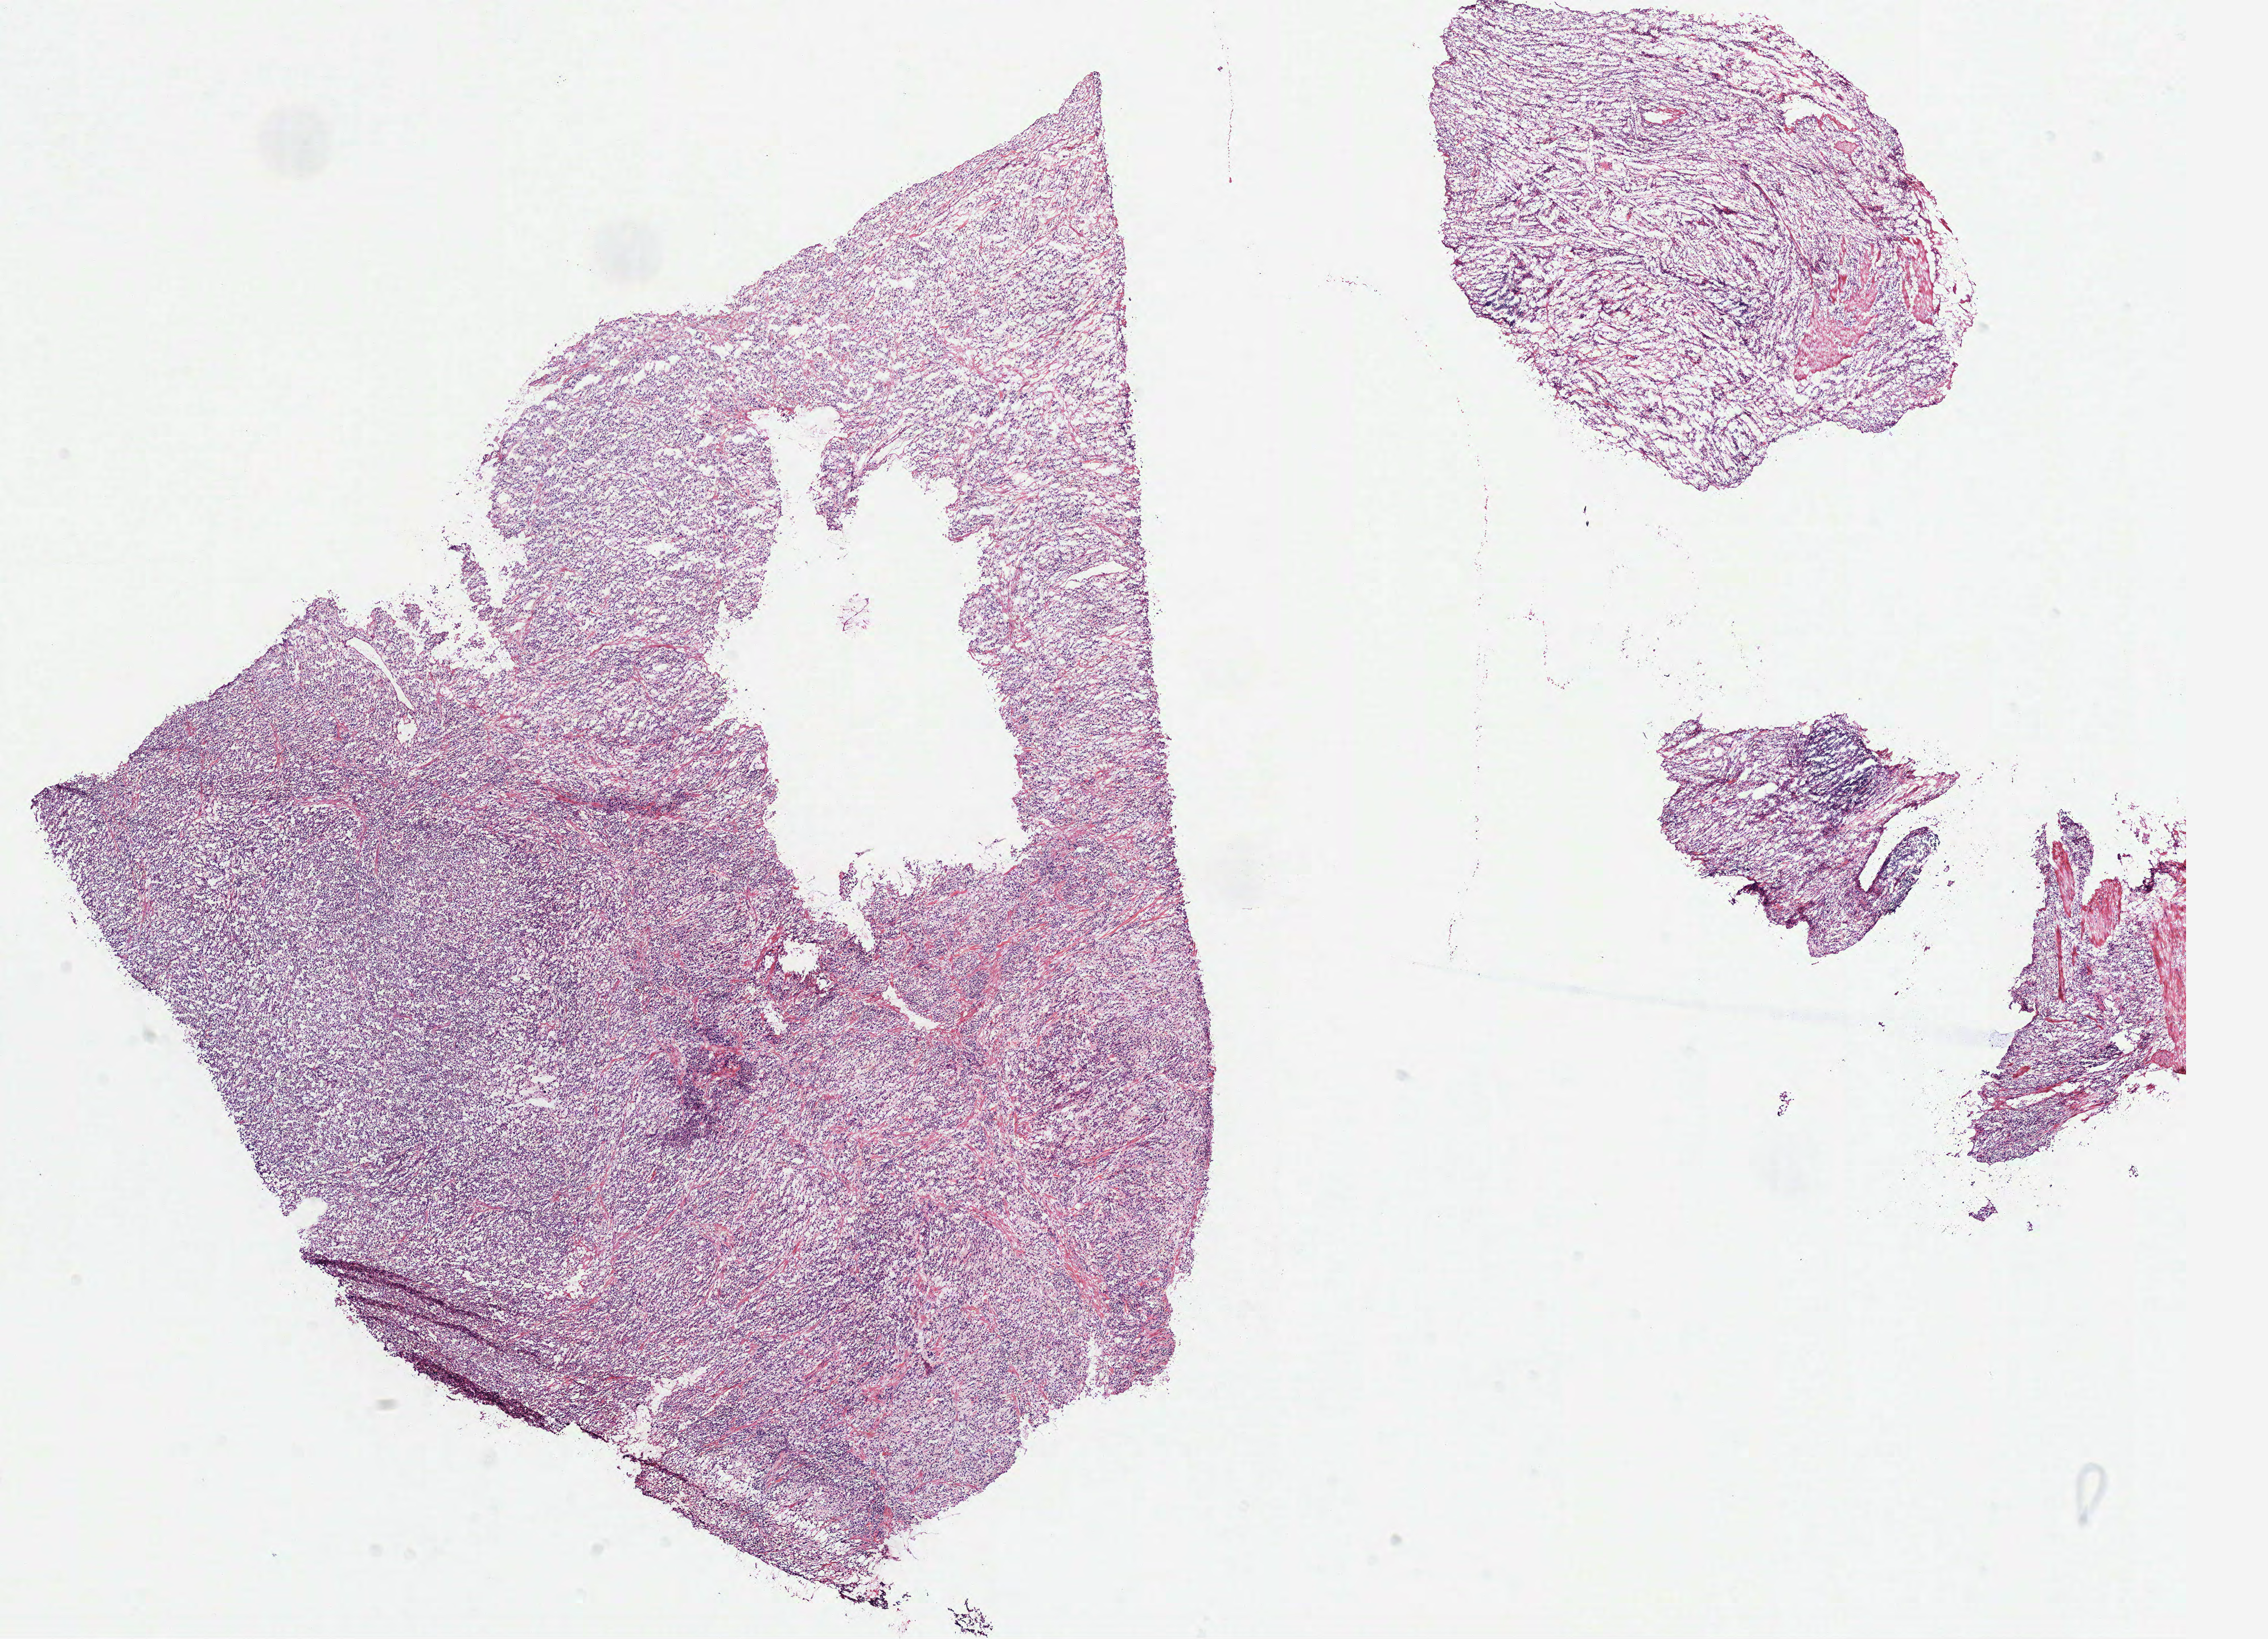
Digitized H&E-stained tissue section (whole slide), a low-resolution overview of the entire scanned area, about 16.1 x 11.6 mm (acquisition: 40x scan); frozen section from the top of the tissue portion; primary tumour sample from the stomach. Male patient; age at initial diagnosis 41 years. Histologic grade: G3 (poorly differentiated). Pathologist review of this section (percent, as recorded): tumour cells 90%, tumour nuclei 80%, normal cells 0%, stromal cells 10%, necrosis 0%.
• AJCC pathologic stage: II (6th edition)
• pathologic diagnosis: Carcinoma, diffuse type